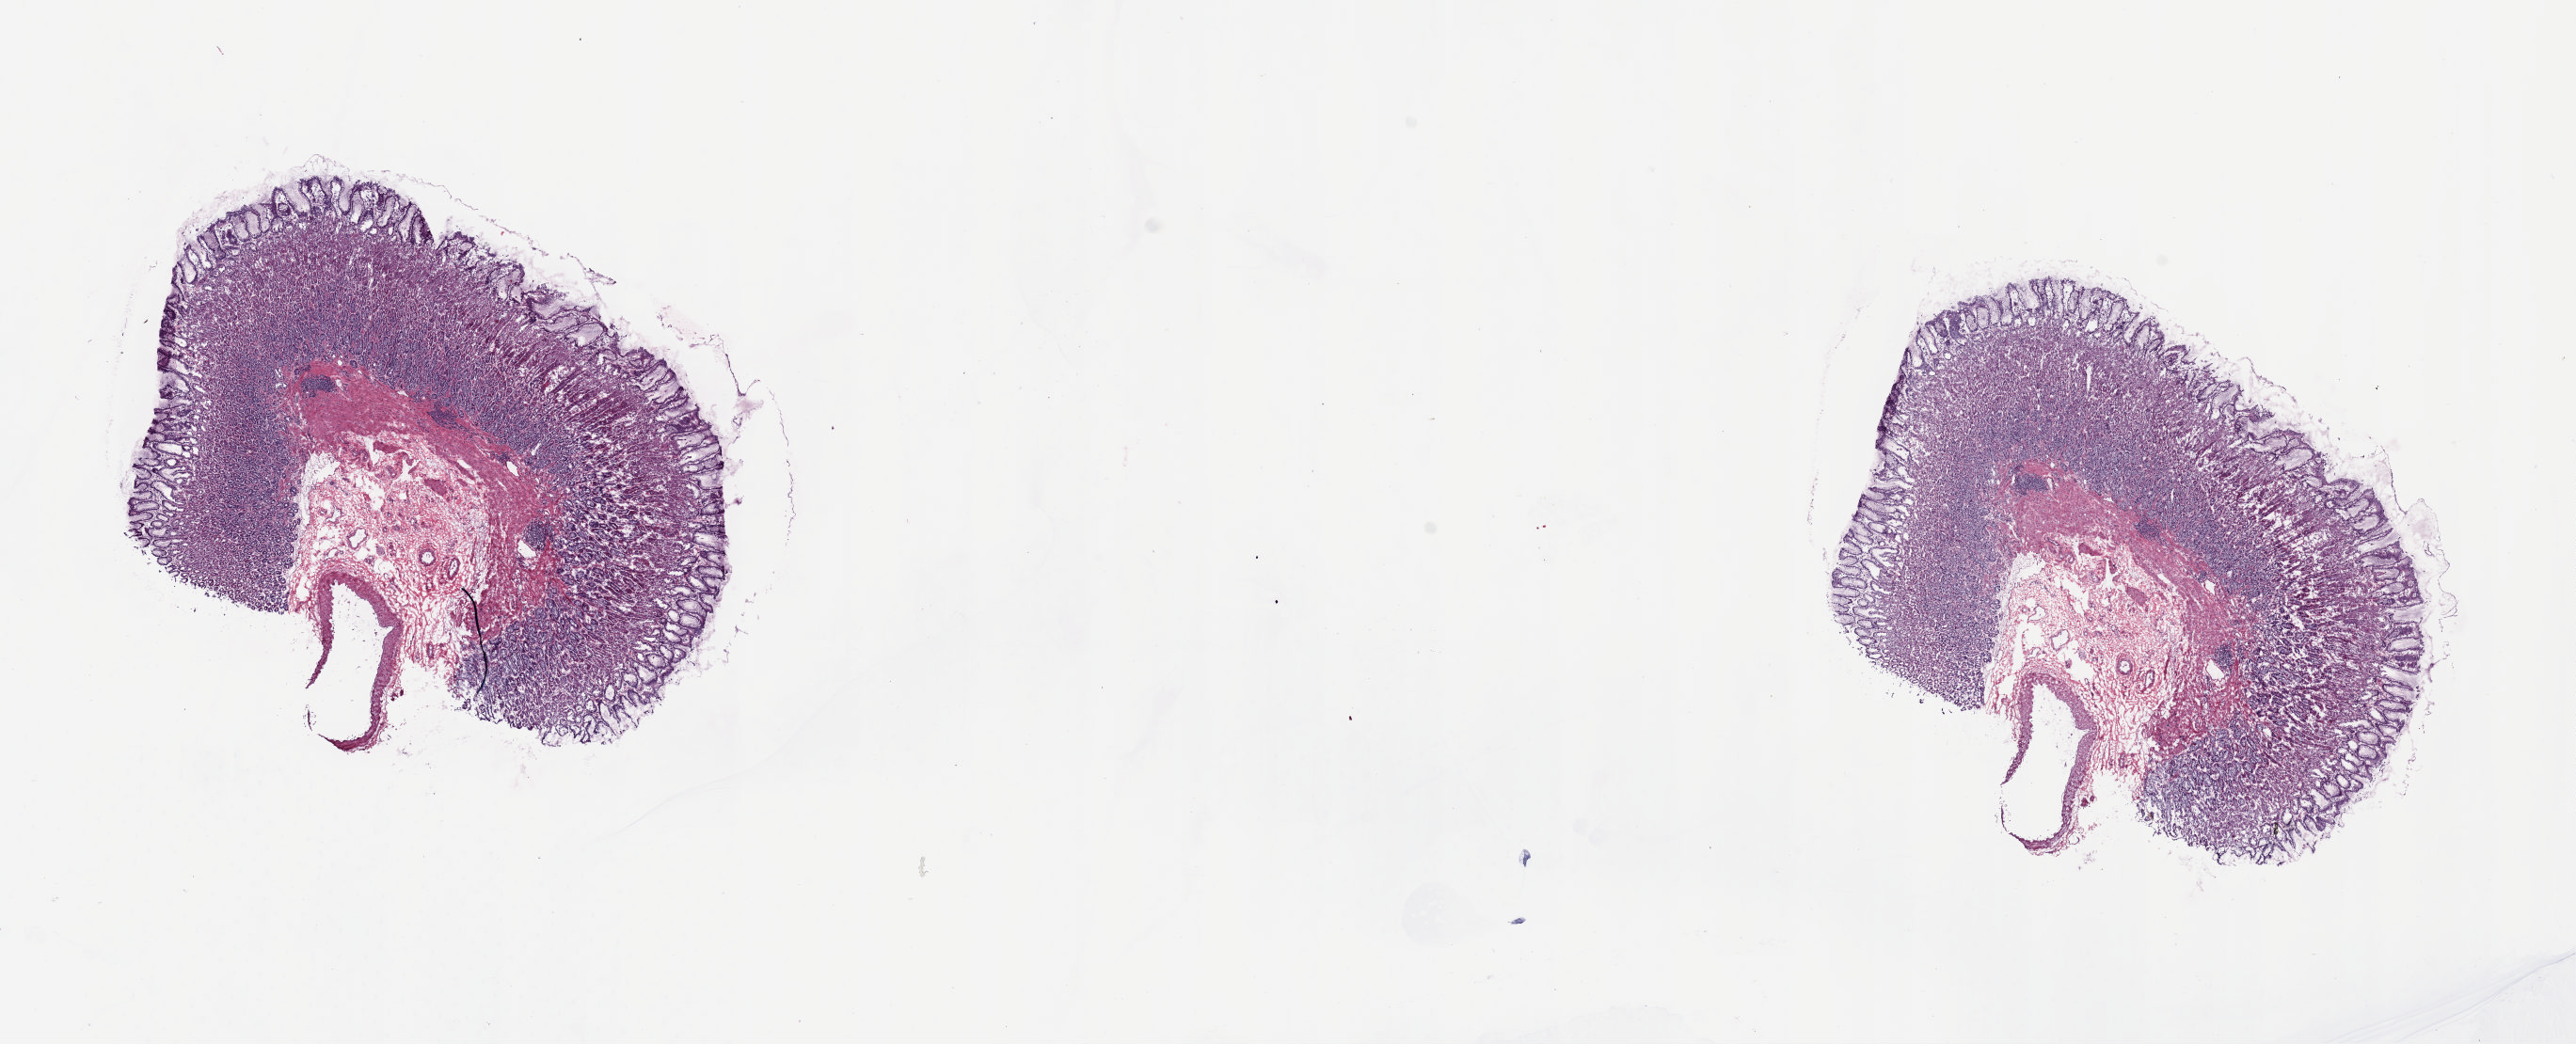
Whole-slide histology image, H&E-stained — whole scanned area (about 21.6 x 8.8 mm) shown as a low-resolution overview, frozen section from the top of the tissue portion, sample: solid tissue normal (non-tumour tissue), esophagus. Patient: female, age at initial diagnosis 70 years. Composition of this section per pathologist review: tumour cells 0%, tumour nuclei 0%, normal cells 100%, stromal cells 0%, necrosis 0%. Infiltration values recorded for this section: lymphocyte infiltration 0%, monocyte infiltration 0%, neutrophil infiltration 0%.
This section: solid tissue normal sample (biorepository sample class). Patient diagnosis: Adenocarcinoma, NOS (lower third of esophagus).